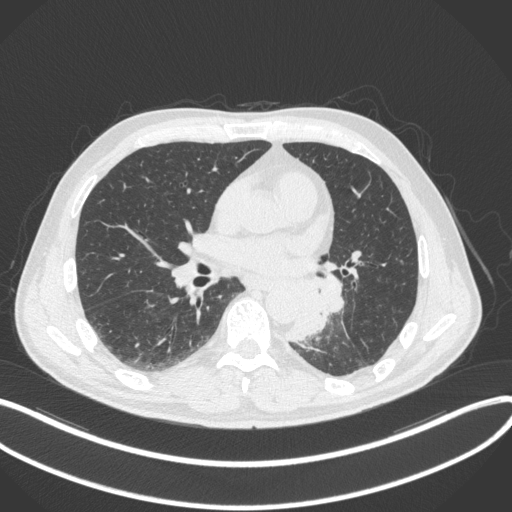
Chest CT, one axial slice; position 162 of 328 along the scan axis; lung window (W 1500 / L -600 HU); 512 × 512 image matrix, field of view 400 × 400 mm. Male patient, age 59 years. Case-level facts recorded for this patient, not image findings: clinical TNM (as recorded): T2a N2 M0.
Outlined on this slice (rectangle marked by the reading radiologist):
- lung tumour (recorded histology: squamous cell carcinoma): box from (x=288, y=271) to (x=348, y=344) px